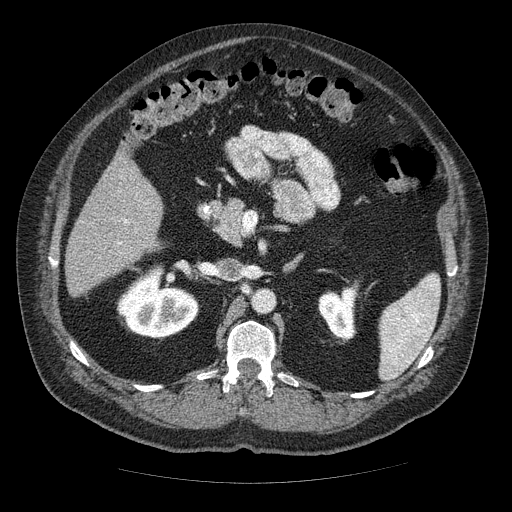
Contrast-enhanced abdominal CT (liver protocol), one axial slice; slice 21 of 85 in the series (ordered by position); reconstruction kernel STANDARD; 120 kVp; soft-tissue window (W 400 / L 40 HU); 512 × 512 image matrix, field of view 420 × 420 mm. Case-level facts recorded for this patient, not image findings: diagnosis: hepatocellular carcinoma (patient treated with transarterial chemoembolisation; whether this scan precedes or follows treatment is not stated here); TNM stage (as recorded): Stage-IIIA; Child-Pugh class: A; tumour nodularity: multinodular; tumour size: 7 cm.
Outlined on this slice (semi-automatically segmented with operator editing):
- liver parenchyma outside the tumour (the mass and vessels are separate outlines, so this box may not span the whole liver): bounding box <64,152,162,296> (left, top, right, bottom; pixels)
- liver vessels: <118,220,128,245>